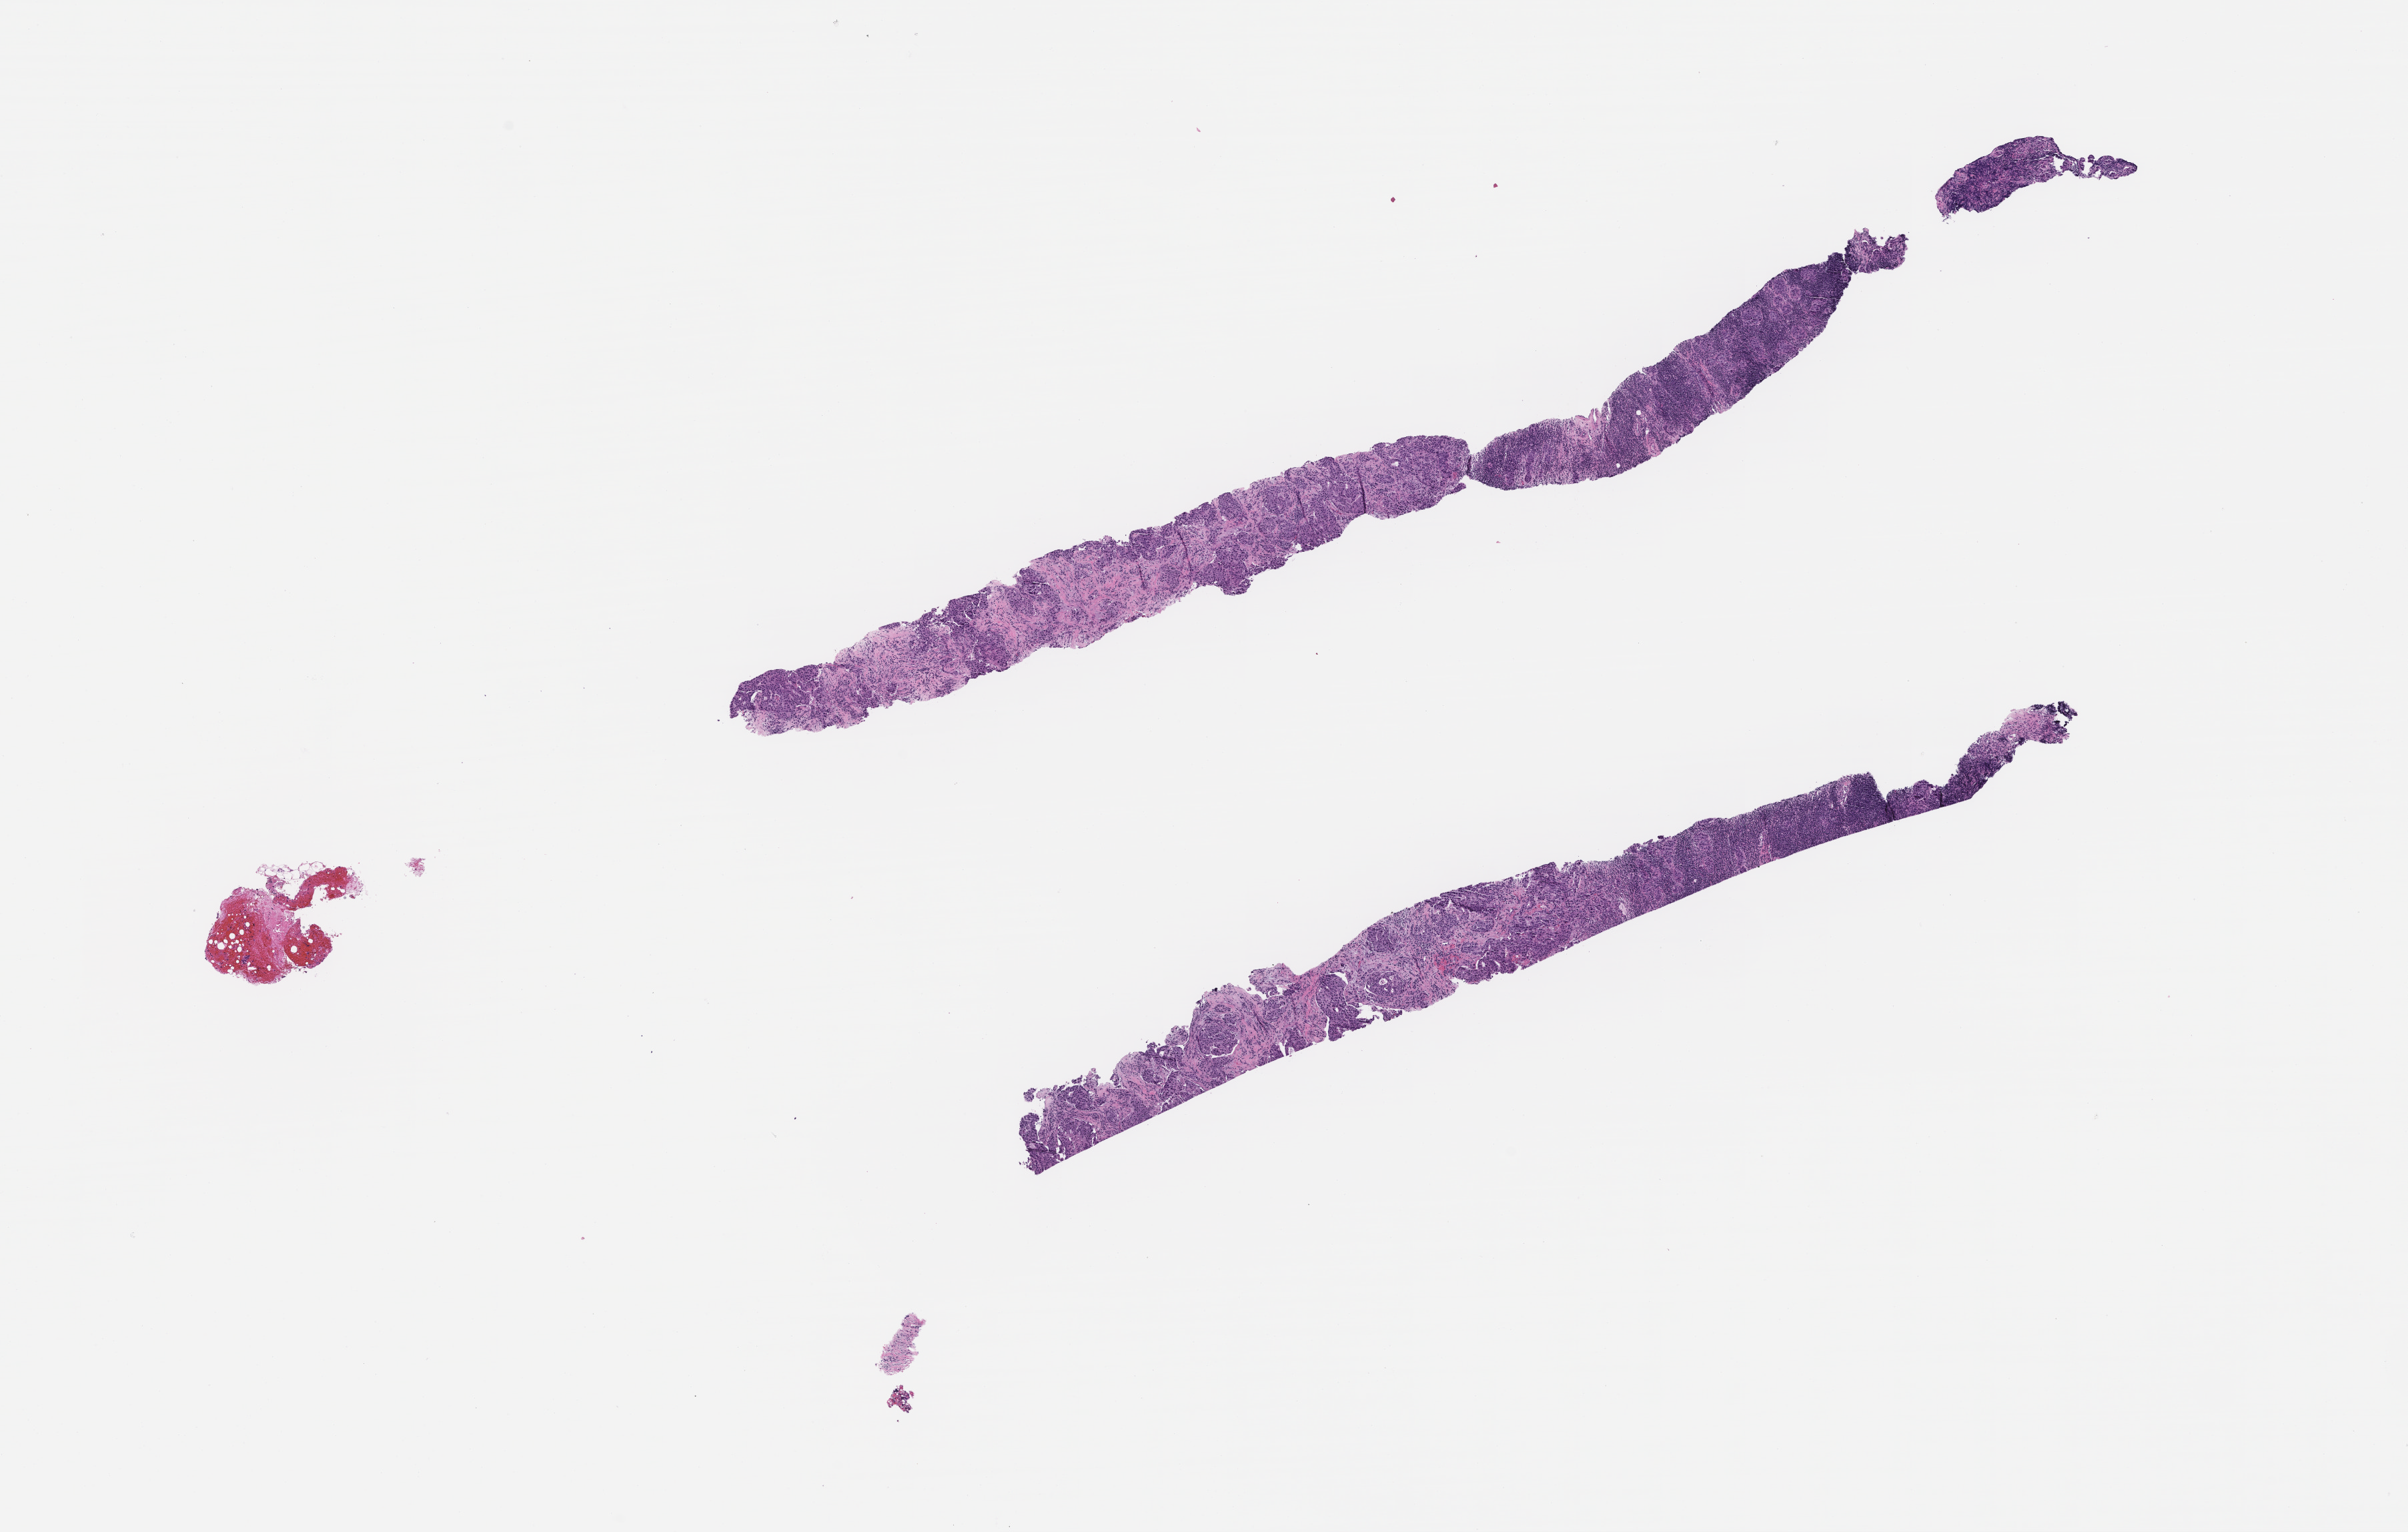
Whole-slide image, hematoxylin and eosin (H&E) stain, a low-resolution overview of the entire scanned area, about 14.6 x 9.3 mm. Formalin-fixed, paraffin-embedded (FFPE) tissue. Patient: female.
This section: metastasis (sampled organ not recorded). Primary diagnosis of the patient: Invasive Breast Carcinoma.